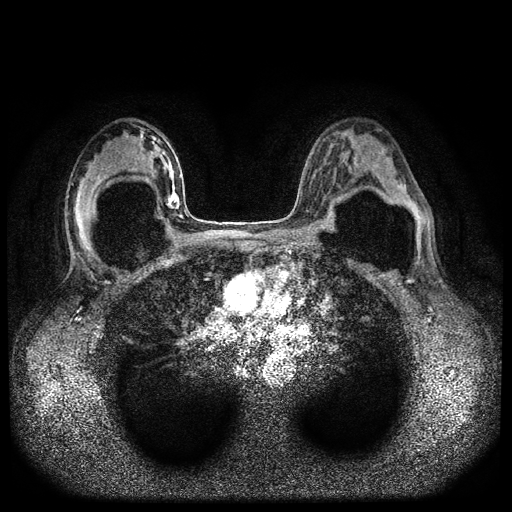
Breast MRI (dynamic contrast-enhanced, multi-phase), one axial slice; slice 57 of 116 in the series (ordered by position); dynamic contrast-enhanced series, time point 2 of 5 at this slice position (early post-contrast); 1.5 T; TE 2.6 ms, TR 5.4 ms; 512 × 512 image matrix. Female patient, age 42 years.
Outlined on this slice (semi-automatic segmentation, software-assisted and operator-edited):
- breast lesion (labelled 'tumour' in the annotation; benign lesions carry a separate 'benign' label): bounding box [x1, y1, x2, y2] px = [164, 186, 182, 212]